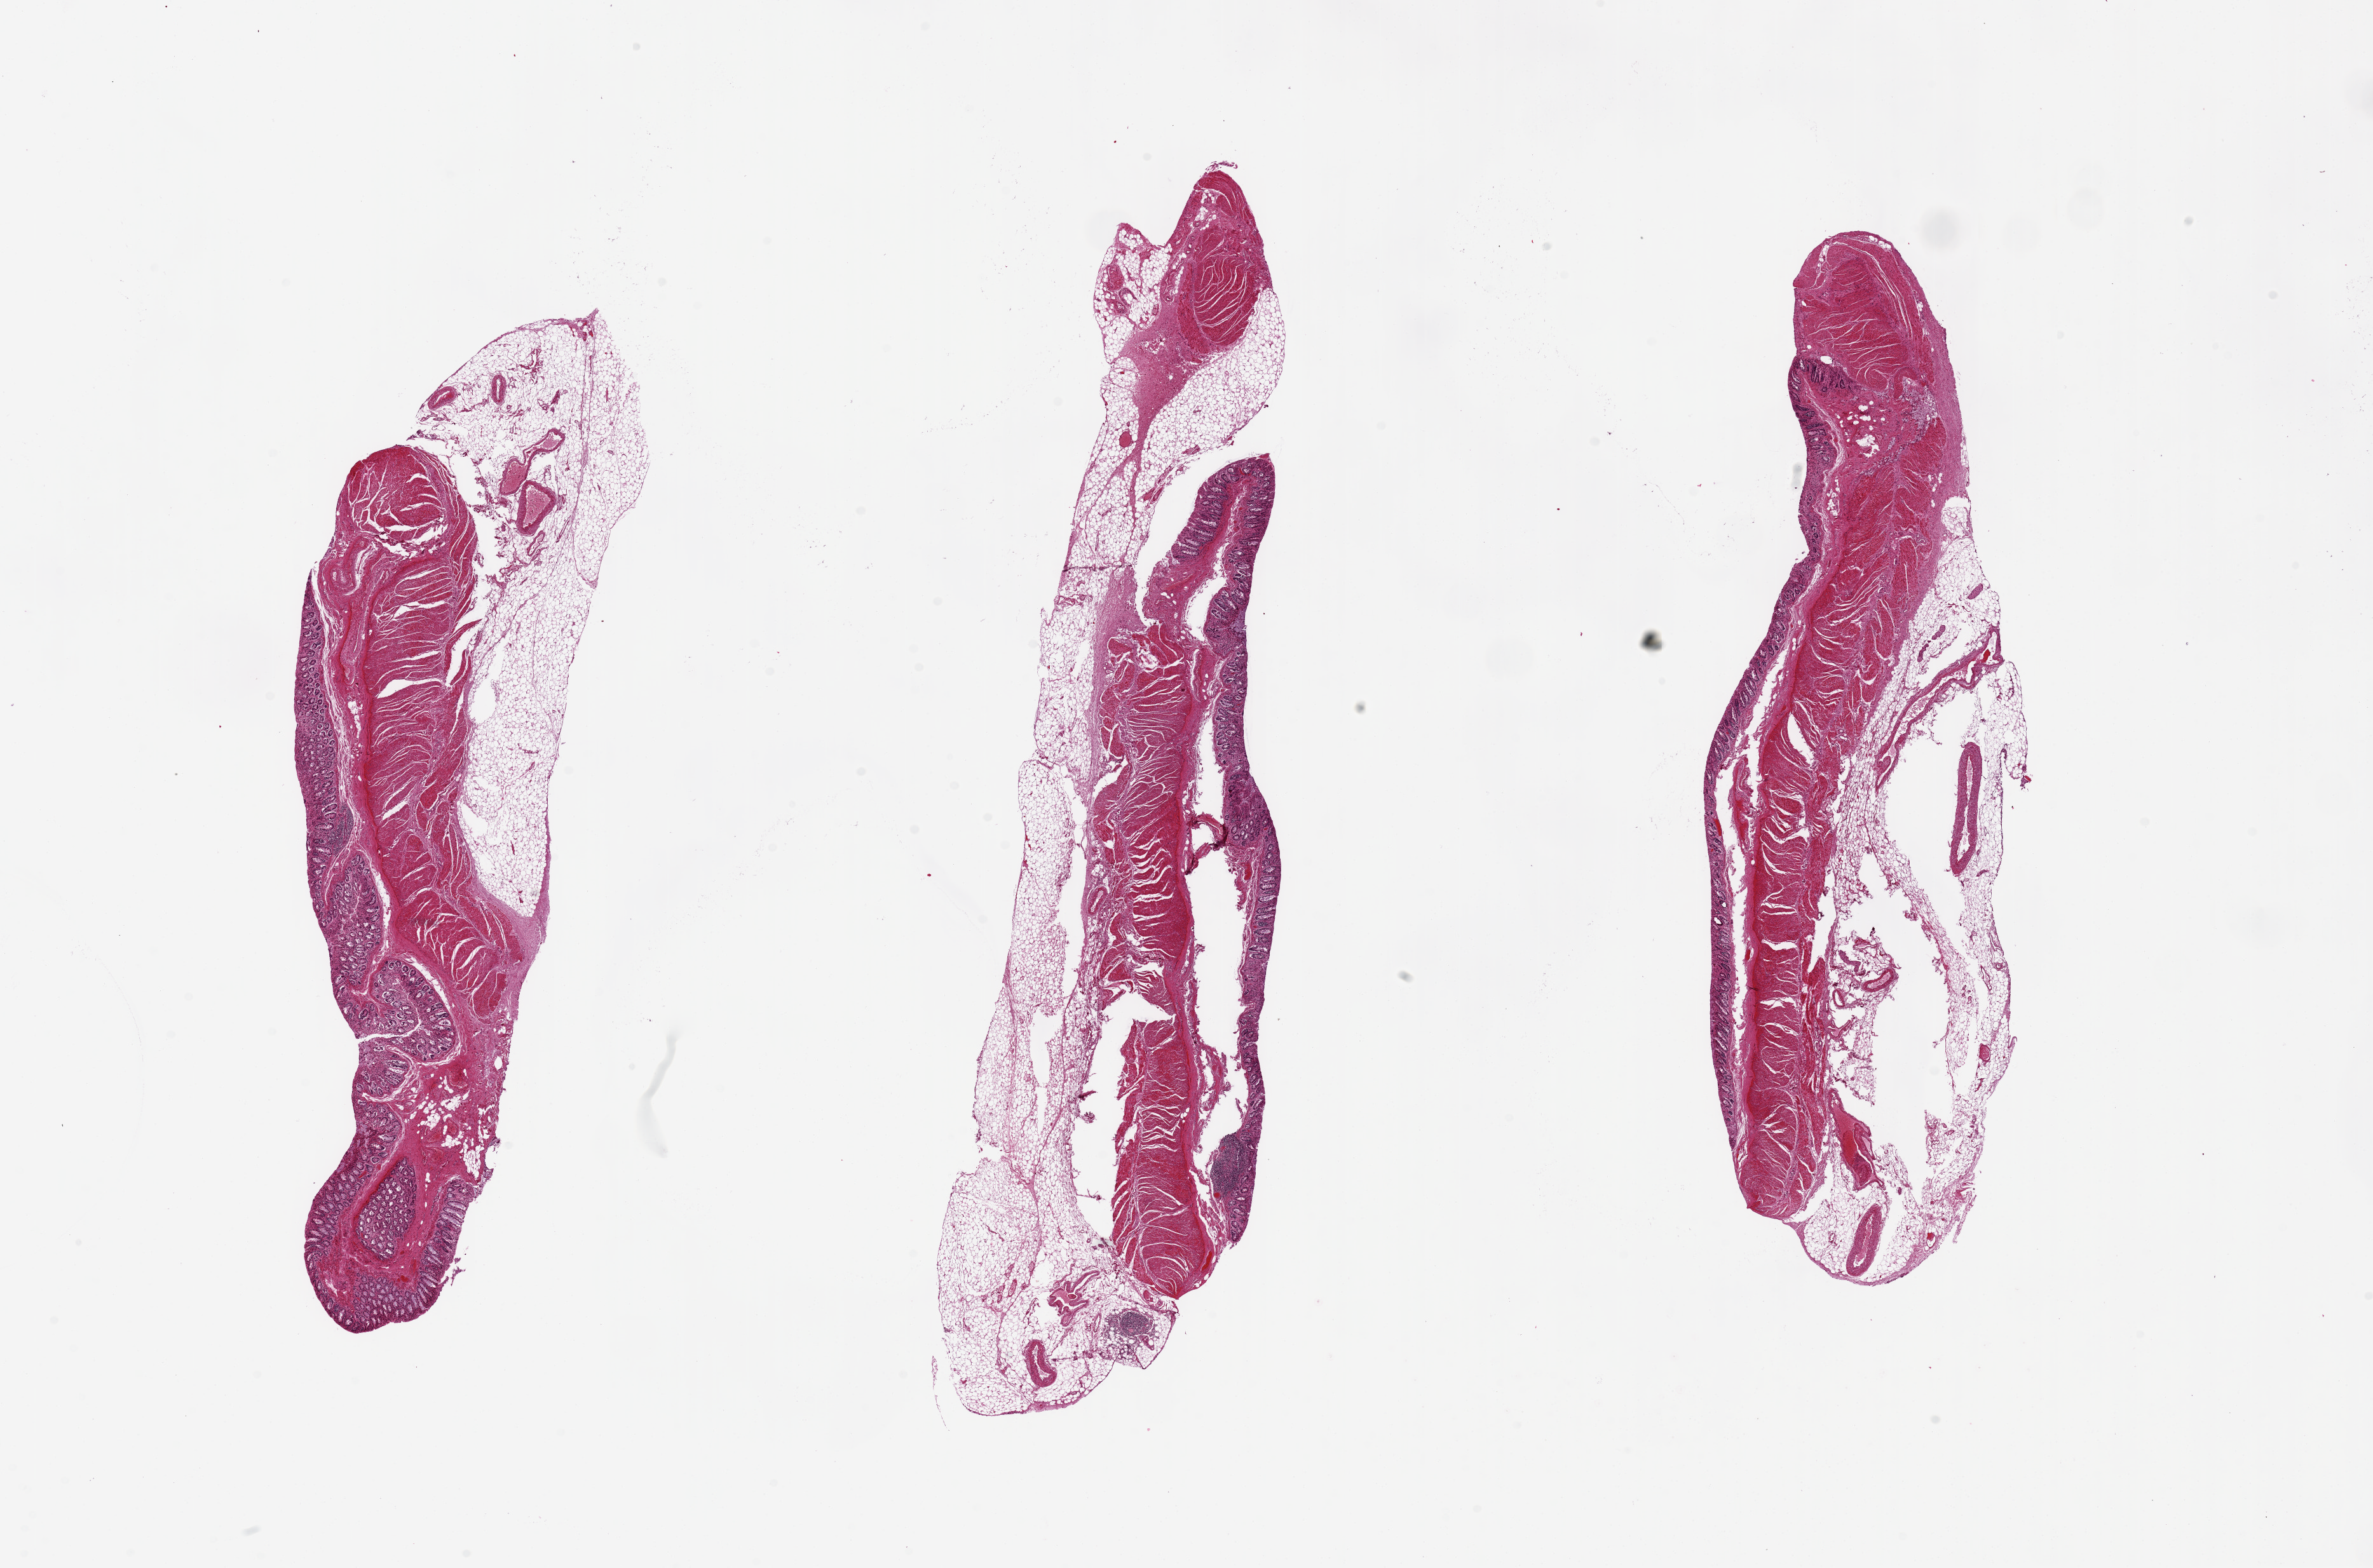
Digitized haematoxylin and eosin-stained section, brightfield — a low-resolution overview of the entire scanned area, about 29.5 x 19.5 mm (acquisition: 20x scan), PAXgene-fixed, paraffin-embedded tissue, section of transverse colon (target tissue), tissue donor sample. Donor sex: female.
Review note (as recorded): 3 pieces 12x3.5 mm.